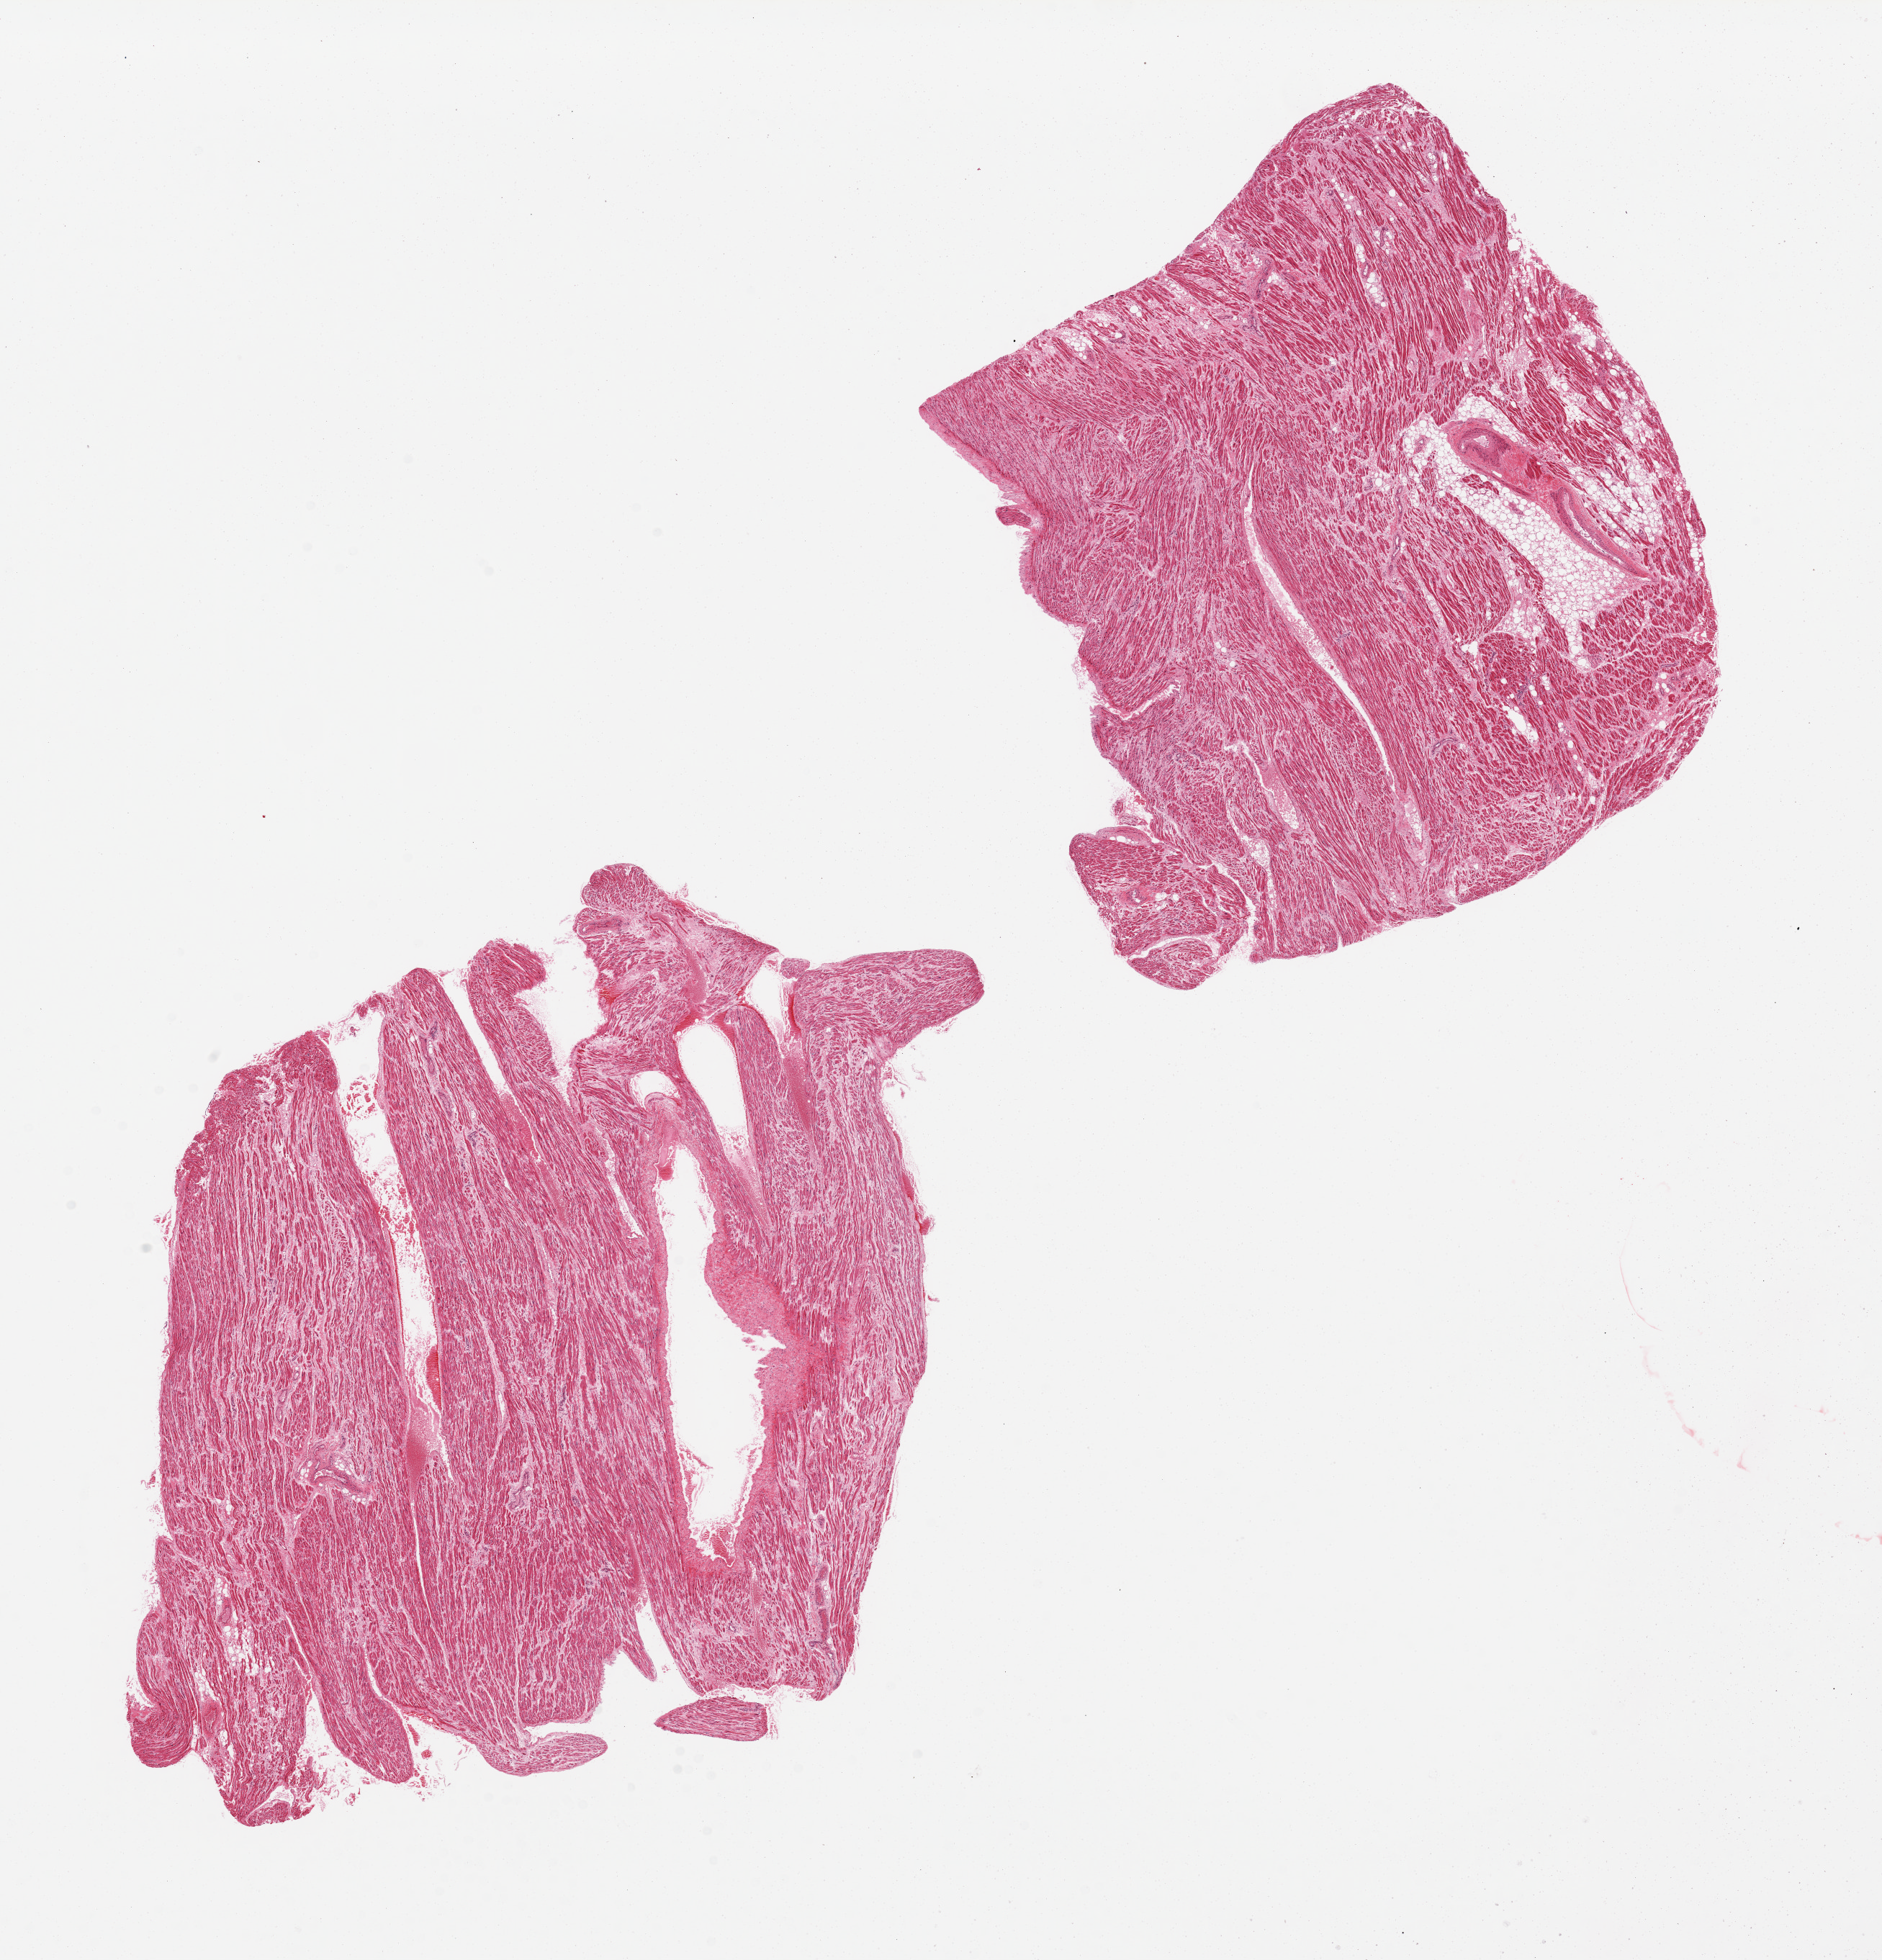
Haematoxylin and eosin whole-slide image, low-resolution overview of the scanned area, about 20.7 x 21.5 mm, PAXgene-fixed, paraffin-embedded tissue, section of auricular appendage (target tissue), tissue donor sample. Donor: female.
* review note (as recorded): 2 pieces, no significant changes